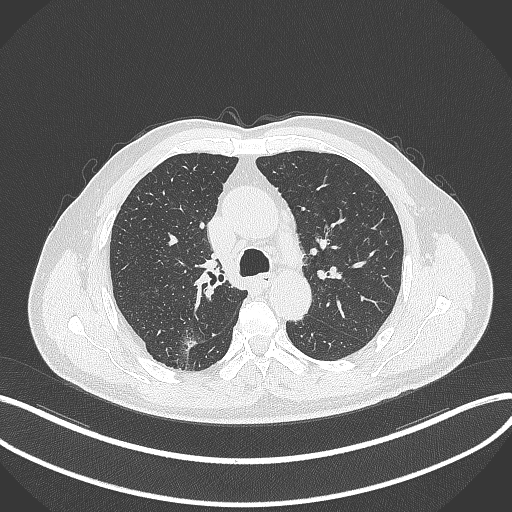
Chest CT, one axial slice. Slice 250 of 359 in the series (ordered by position). Reconstruction kernel B70f. 120 kVp. Lung window (W 1500 / L -600 HU). 1 mm slice thickness. 512 × 512 image matrix, field of view 400 × 400 mm. Patient: male, 69 years. Case-level facts recorded for this patient, not image findings: clinical TNM (as recorded): T1b N0 M0; histopathological grade: G2-3.
Structures marked on this image (bounding box drawn by a radiologist):
- lung tumour (recorded histology: adenocarcinoma): box from (x=182, y=336) to (x=198, y=355) px